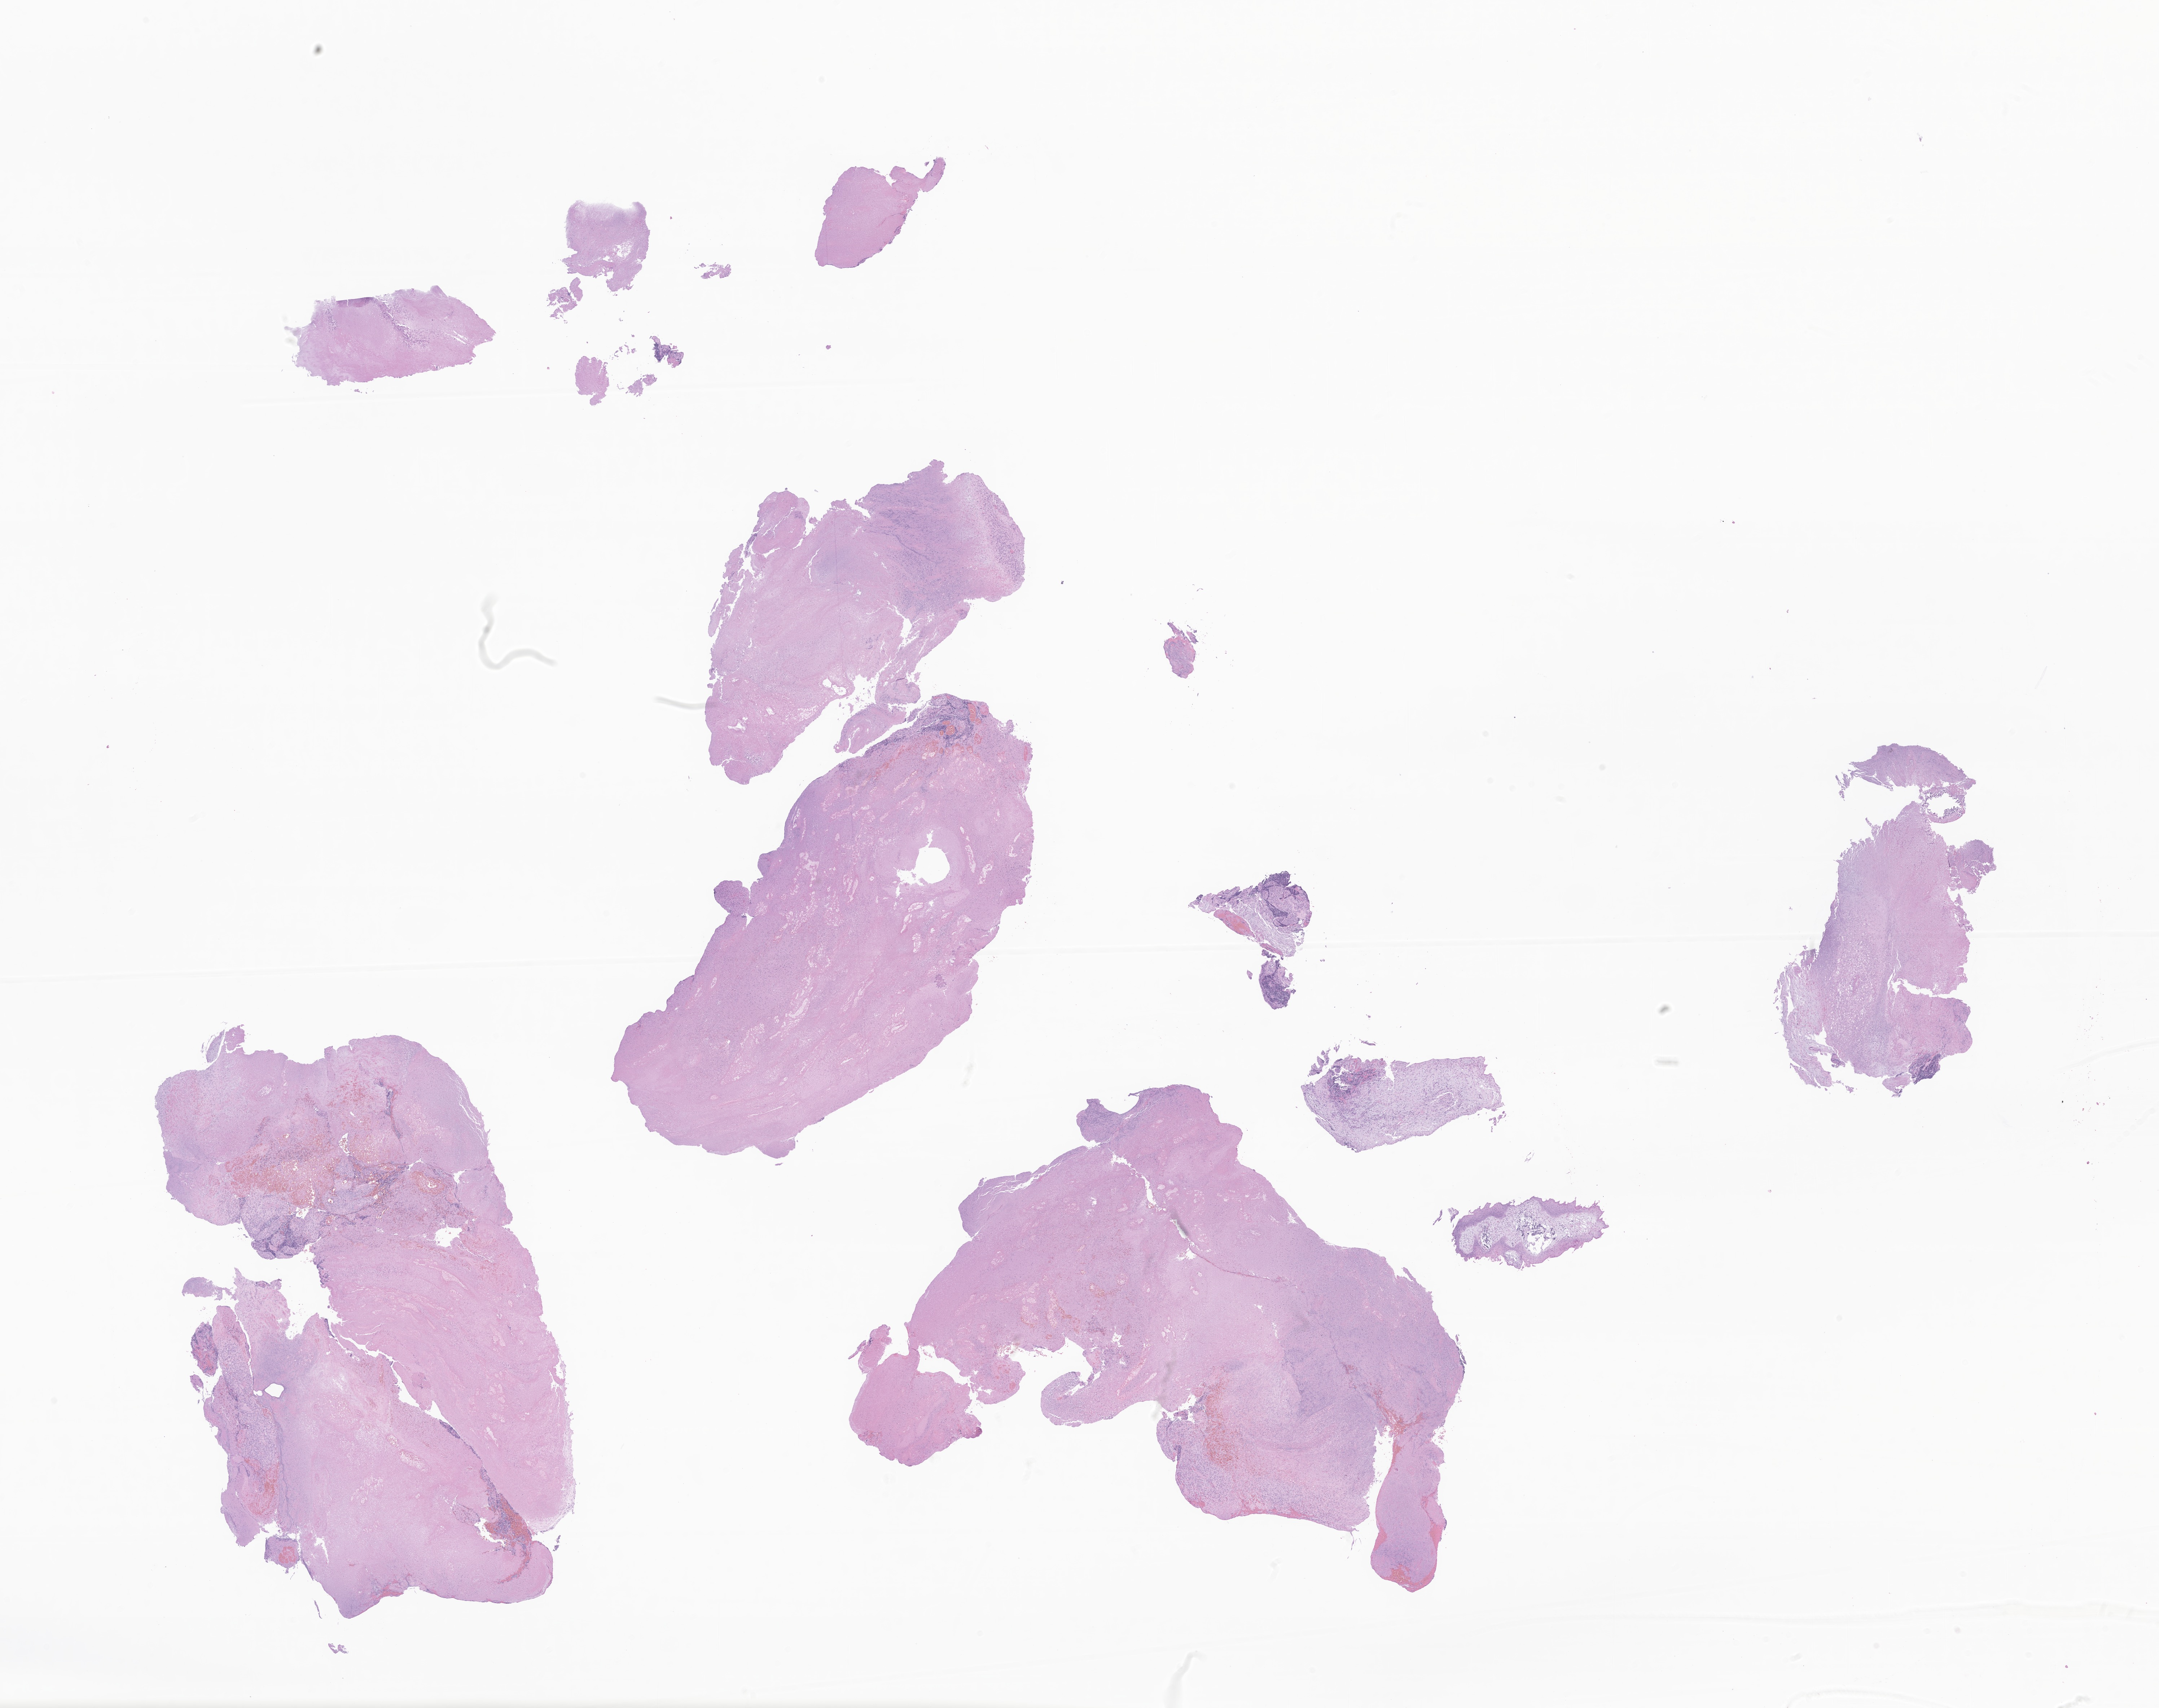
H&E whole-slide image of tumor tissue from the nasal cavity, shown as a low-resolution overview of the whole scanned area (about 25.2 x 20.0 mm); FFPE section. Patient: male, age 61 months.
Recorded diagnosis: Olfactory neuroblastoma.